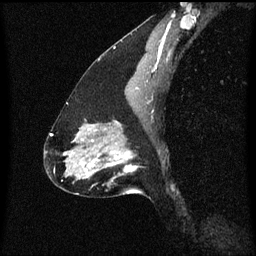
Breast MRI (dynamic contrast-enhanced), one sagittal slice. Slice 38 of 60 in the series (ordered by position). Dynamic contrast-enhanced series, image 2 of 3 at this slice position (ordered by acquisition). 1.5 T. TE 4.2 ms, TR 8.4 ms. 2 mm slice thickness. 256 × 256 image matrix, field of view 200 × 200 mm. Female patient, age 47 years.
Structures marked on this image (semi-automatically segmented with operator editing):
- analysis volume of interest (the breast-tissue region the enhancement analysis was run in; not a lesion): bounding box (x1, y1, x2, y2) in pixels: (85, 136, 144, 195)
- tumour enhancement mask (voxels above the 70 % enhancement threshold inside the analysis volume of interest): (85, 140, 137, 173)